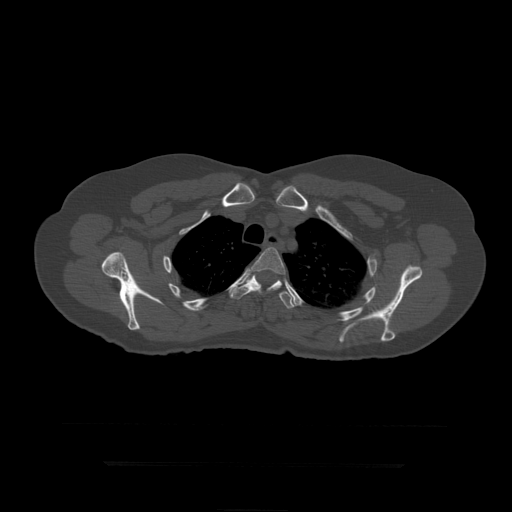
CT including the spine, one axial slice; position 343 of 399 along the scan axis; bone window (W 1800 / L 400 HU); 512 × 512 image matrix. Patient age 41 years. Case-level facts recorded for this patient, not image findings: primary cancer: breast.
Outlined on this slice (semi-automatically segmented with operator editing):
- T4 vertebra: box from (x=247, y=248) to (x=286, y=294) px
- T5 vertebra: (x=227, y=271)–(x=295, y=309)